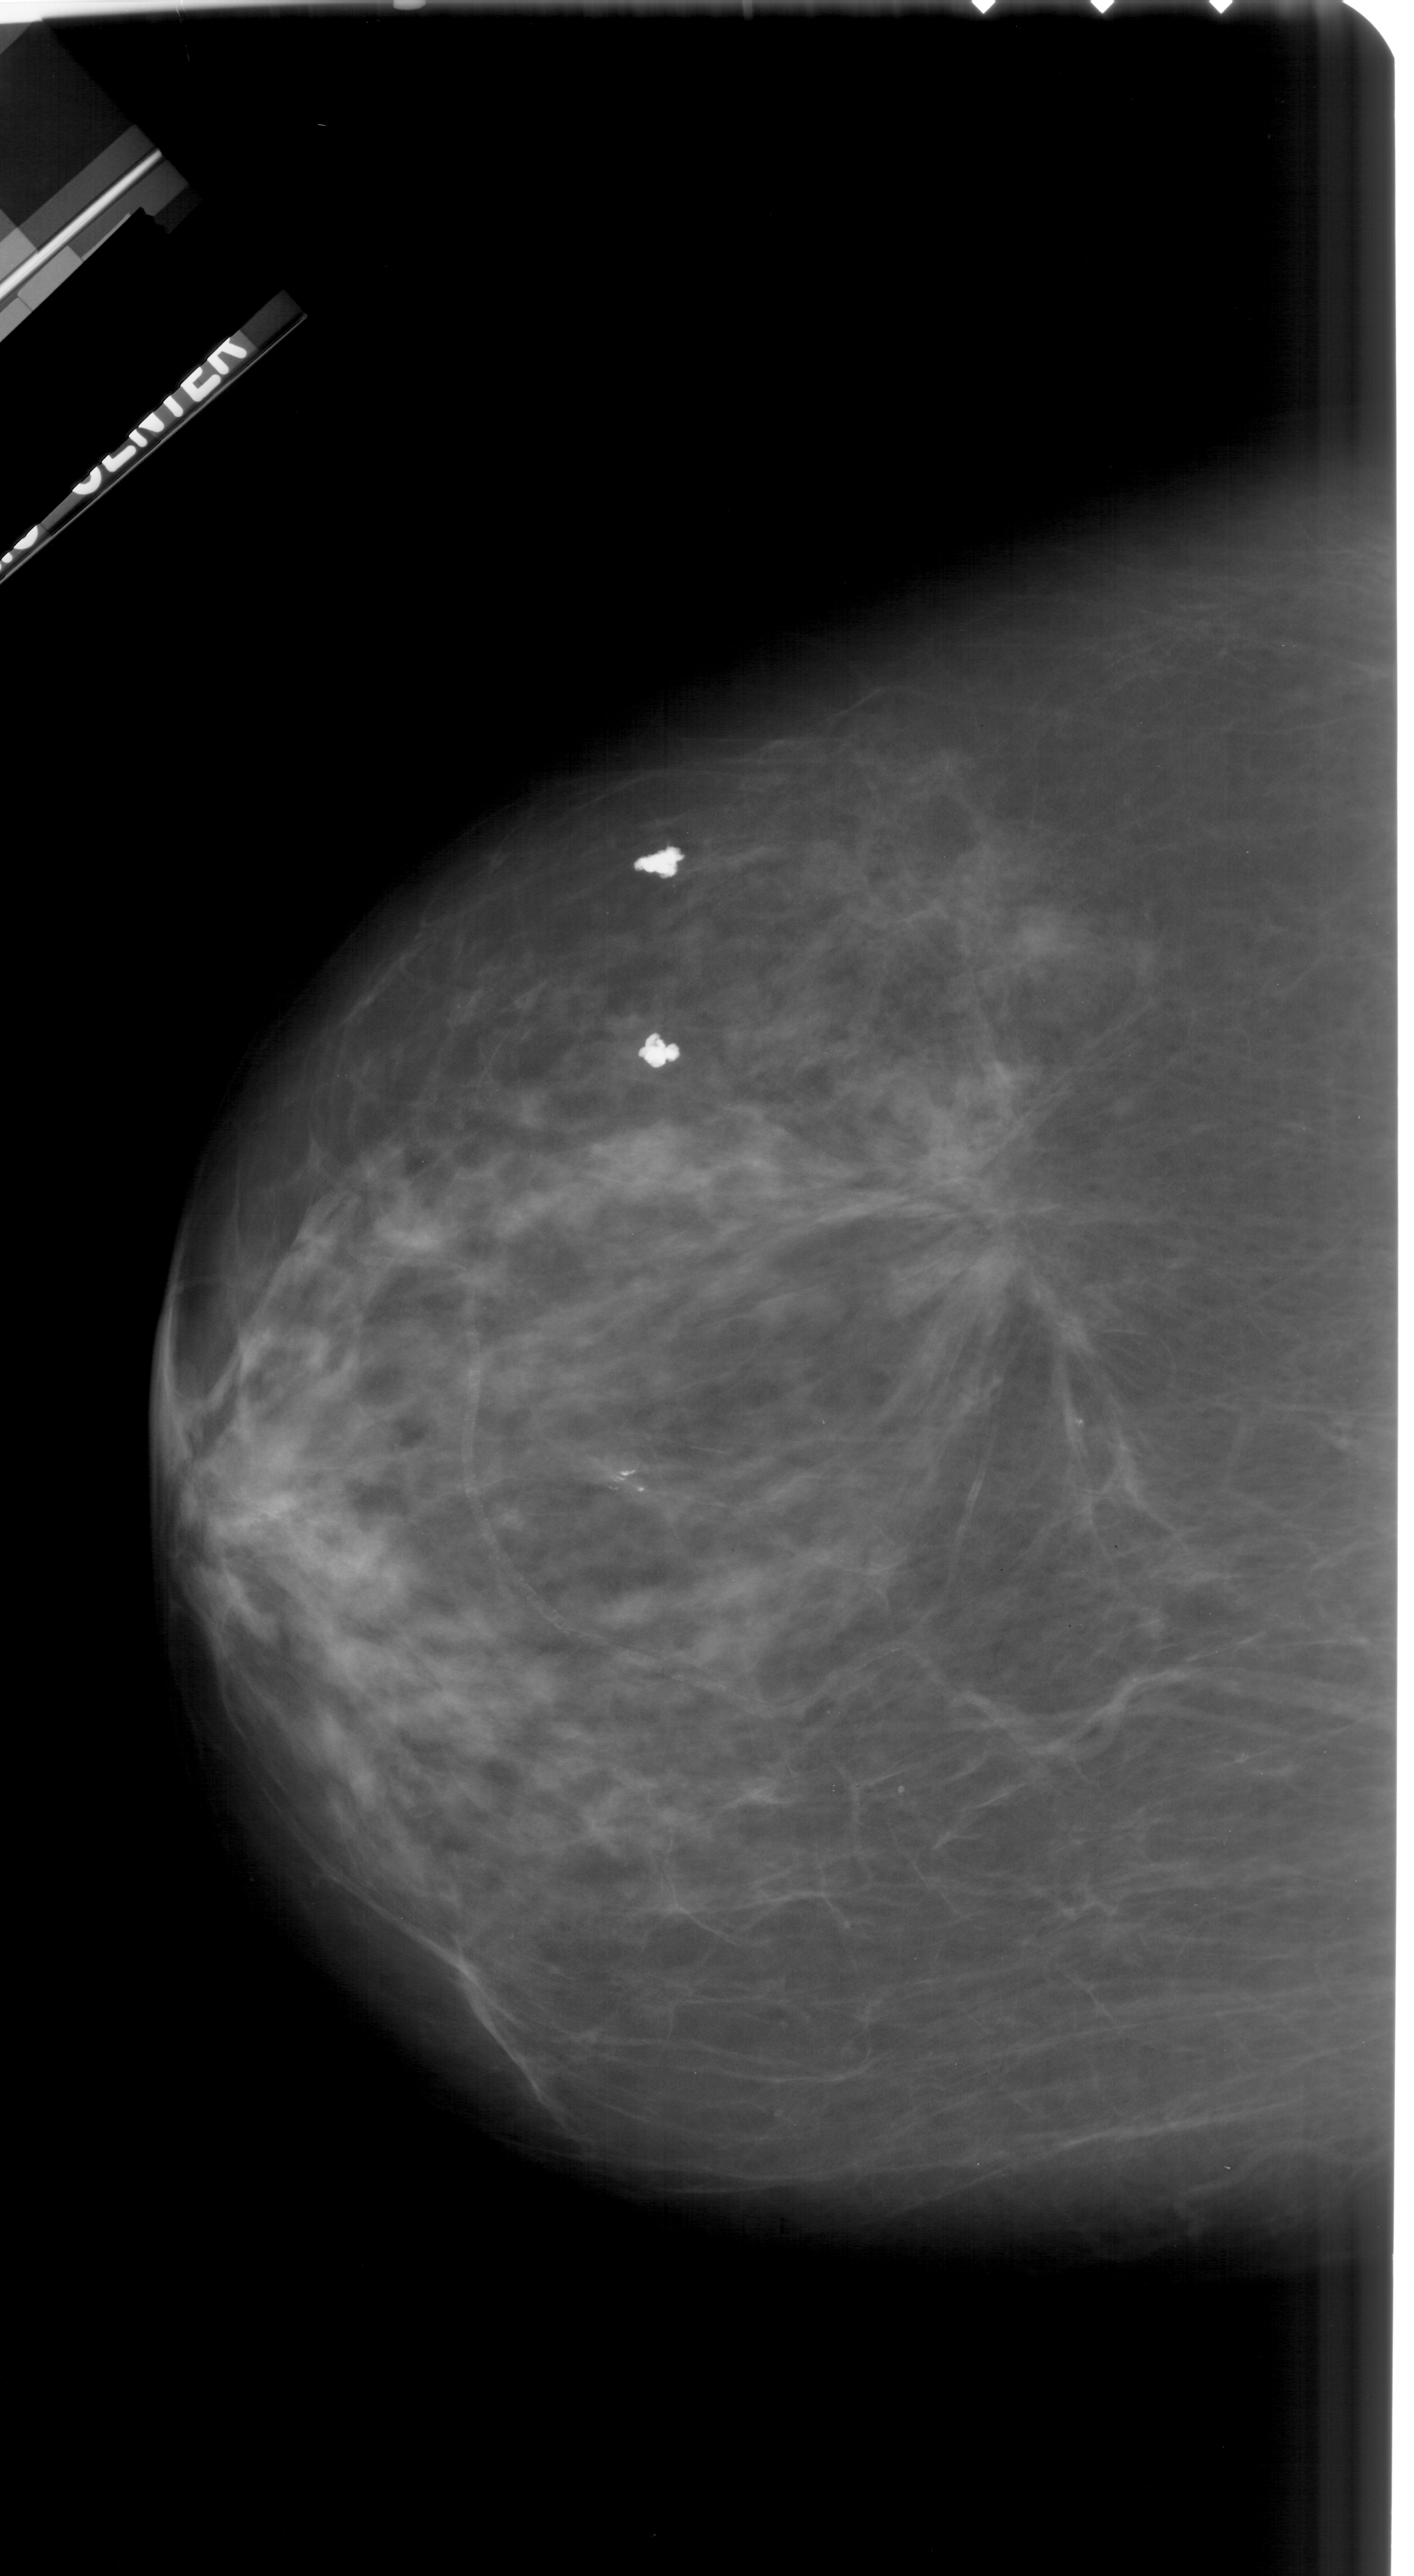
Digitized screen-film mammogram; left breast; CC view; breast composition: scattered fibroglandular densities (BI-RADS density category 2 of 4).
- Abnormality record for this image: mass, shape architectural distortion, margins spiculated; BI-RADS assessment category 5; pathology (as recorded): malignant.